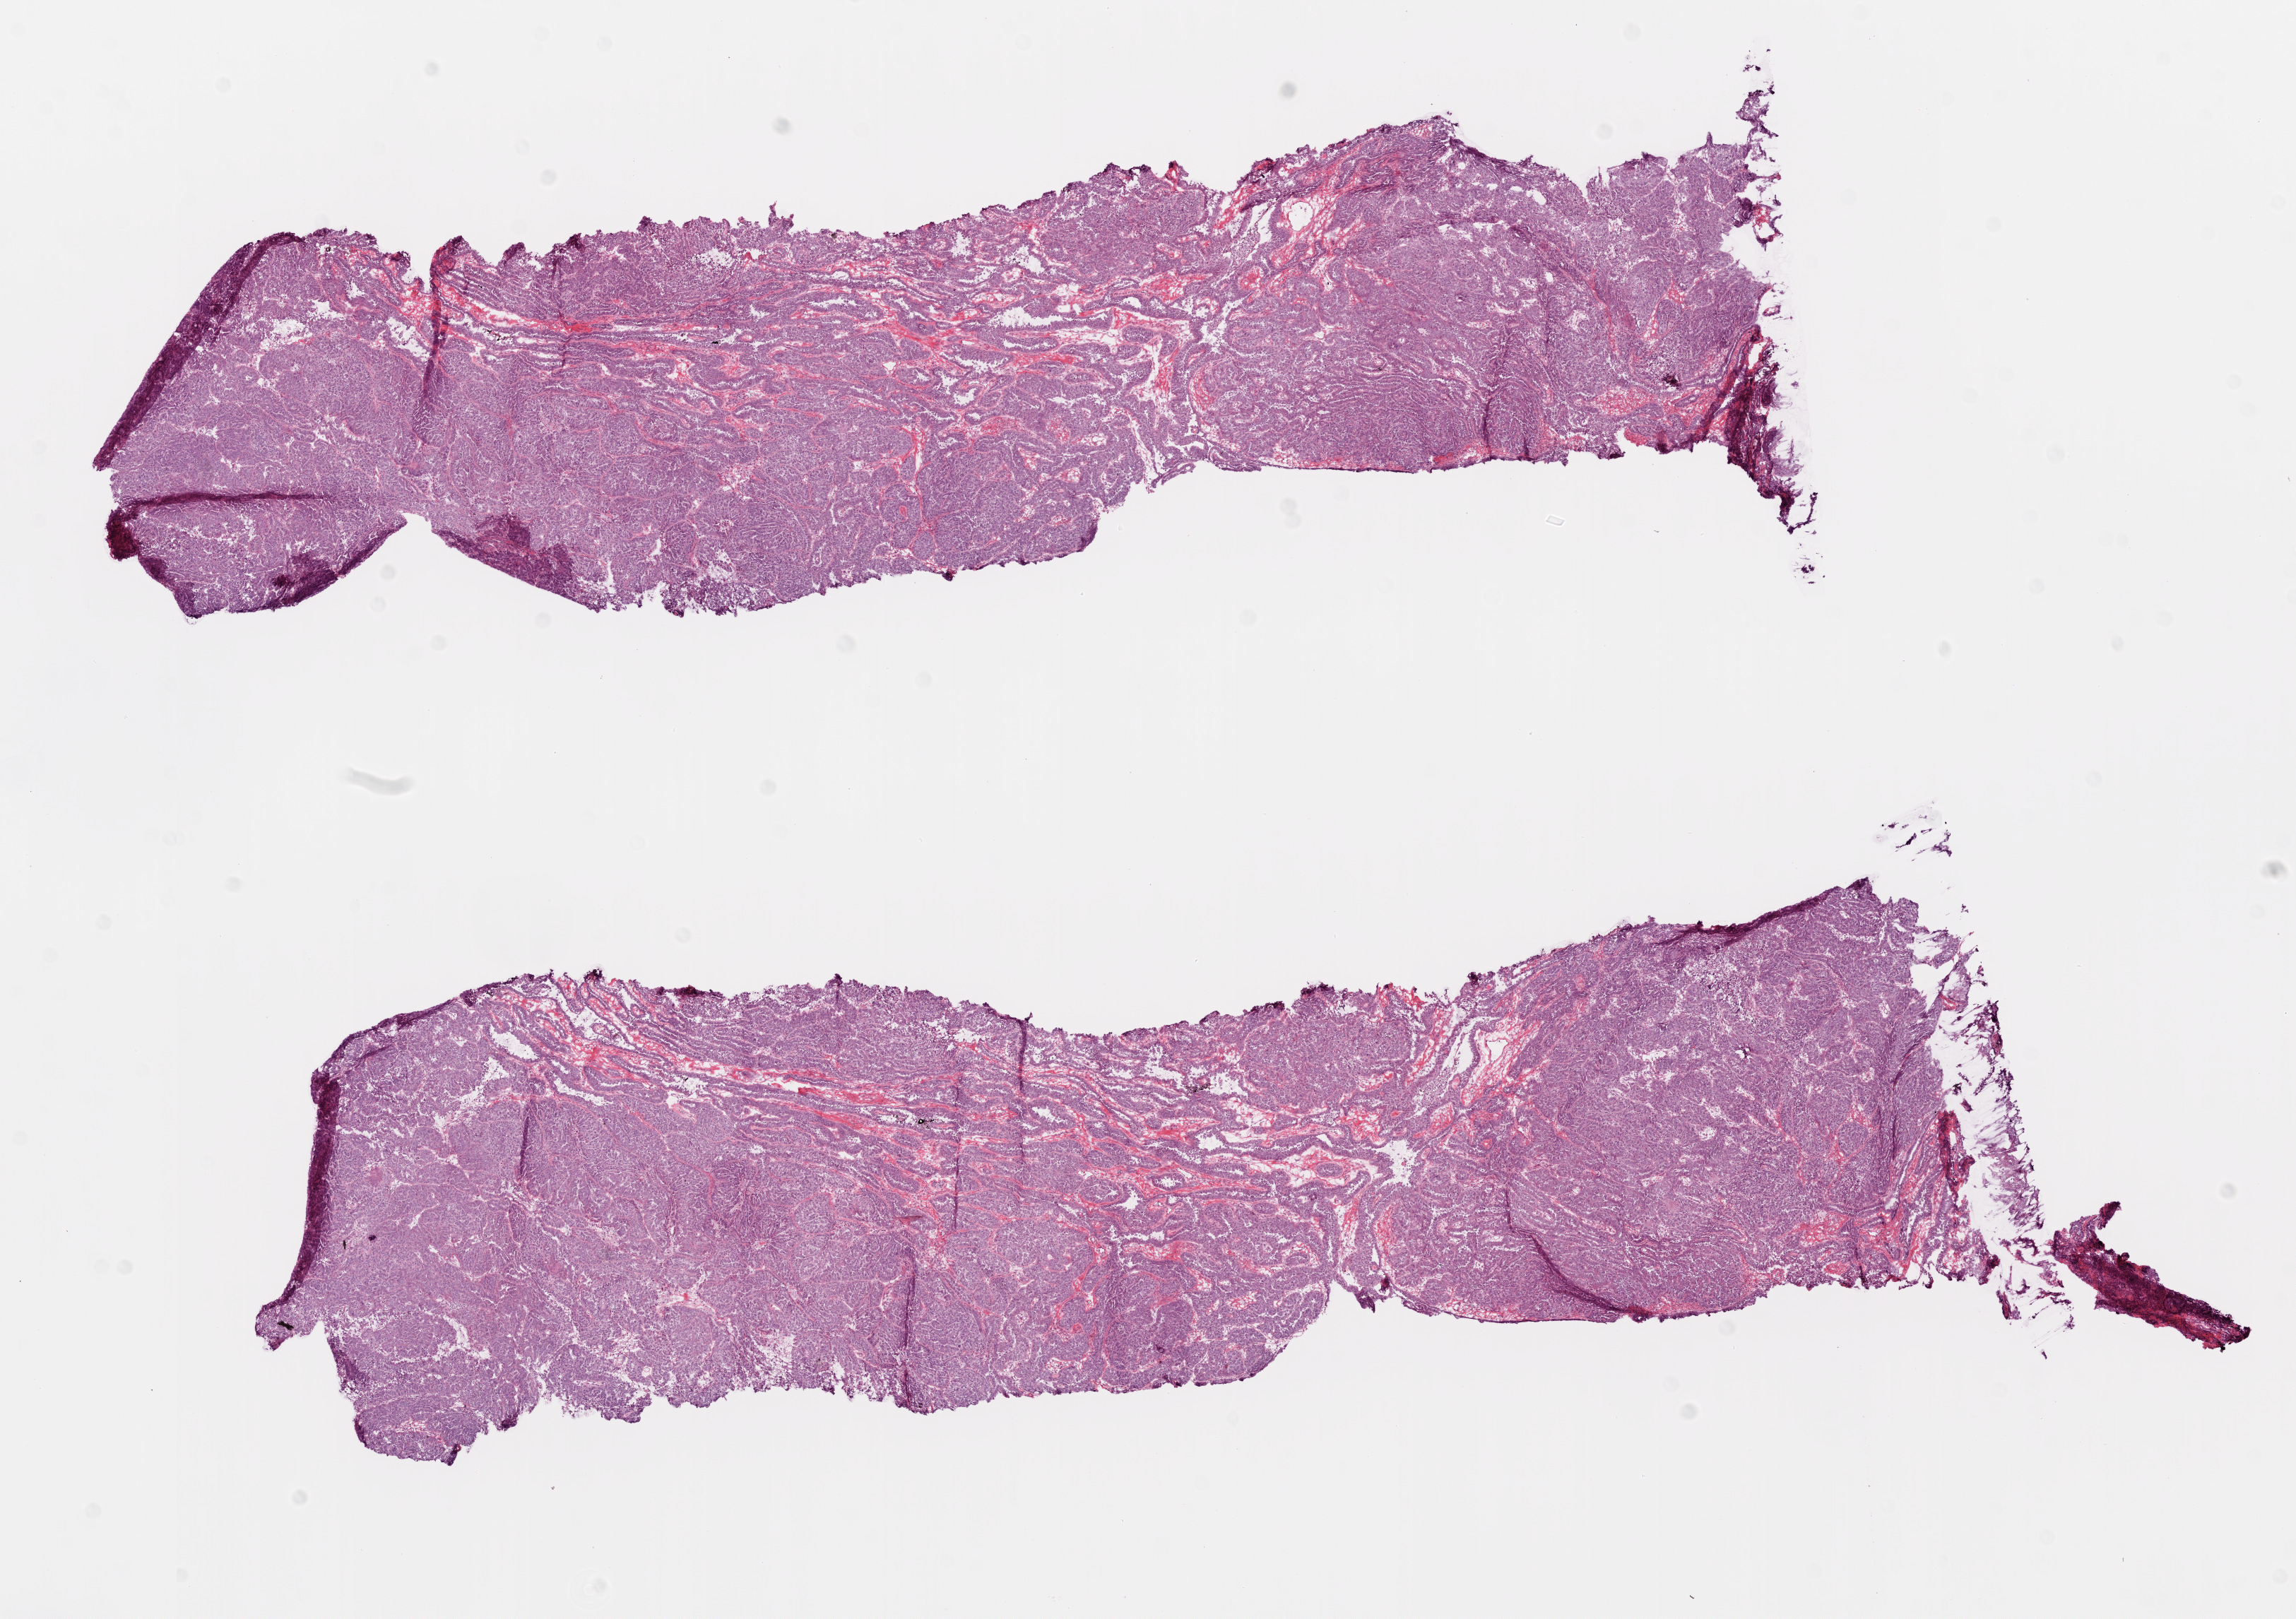
Whole-slide histology image, H&E-stained, whole scanned area (about 13.0 x 9.2 mm, acquisition: 20x scan) shown as a low-resolution overview; frozen section; primary tumour sample from the ovary. Patient: female, age at initial diagnosis 57 years. Histologic grade: G3 (poorly differentiated). Pathologist review of this section (percent, as recorded): tumour cells 95%, tumour nuclei 99%, normal cells 0%, stromal cells 5%, necrosis 0%.
- FIGO stage: IIIA
- histologic diagnosis: Serous cystadenocarcinoma, NOS